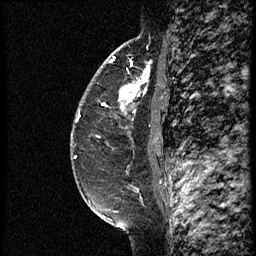
Breast MRI (dynamic contrast-enhanced), one sagittal slice; dynamic contrast-enhanced study with each time point stored as its own series, time point 2 of 3 at this slice position (early post-contrast, ordered by acquisition time); 1.5 T; TE 4.2 ms, TR 18.9 ms; 2 mm slice thickness; 256 × 256 image matrix, field of view 200 × 200 mm. Female patient. From the clinical record (not read from this slice): setting: breast cancer imaged before/during neoadjuvant chemotherapy; receptor status: HER2-positive.
Annotated regions visible in this slice (semi-automatic segmentation, software-assisted and operator-edited):
- analysis volume of interest (the breast-tissue region the enhancement analysis was run in; not a lesion): box from (x=77, y=64) to (x=161, y=147) px
- tumour enhancement mask (voxels above the 100 % enhancement threshold inside the analysis volume of interest): (x=104, y=71)–(x=149, y=115)